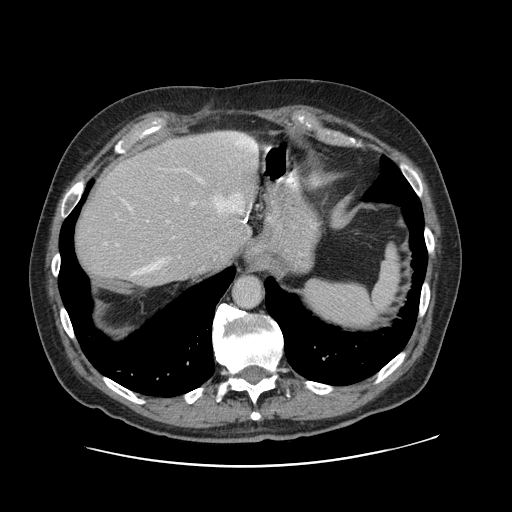
Contrast-enhanced abdominal CT, one axial slice. Position 94 of 138 along the scan axis. 120 kVp. Intravenous contrast given. Soft-tissue window (W 400 / L 40 HU). 512 × 512 image matrix, field of view 402 × 402 mm. Male patient, age 71 years. Case-level facts recorded for this patient, not image findings: diagnosis: colorectal cancer liver metastases, imaged before liver resection; multiple liver metastases: no; largest metastasis: 3.3 cm; disease in both lobes: no.
Outlined on this slice (manually delineated by an expert):
- hepatic veins: bounding box (x1, y1, x2, y2) in pixels: (133, 178, 250, 275)
- liver: (74, 132, 258, 287)
- planned liver remnant (the part of the liver to remain after resection): (74, 156, 238, 288)